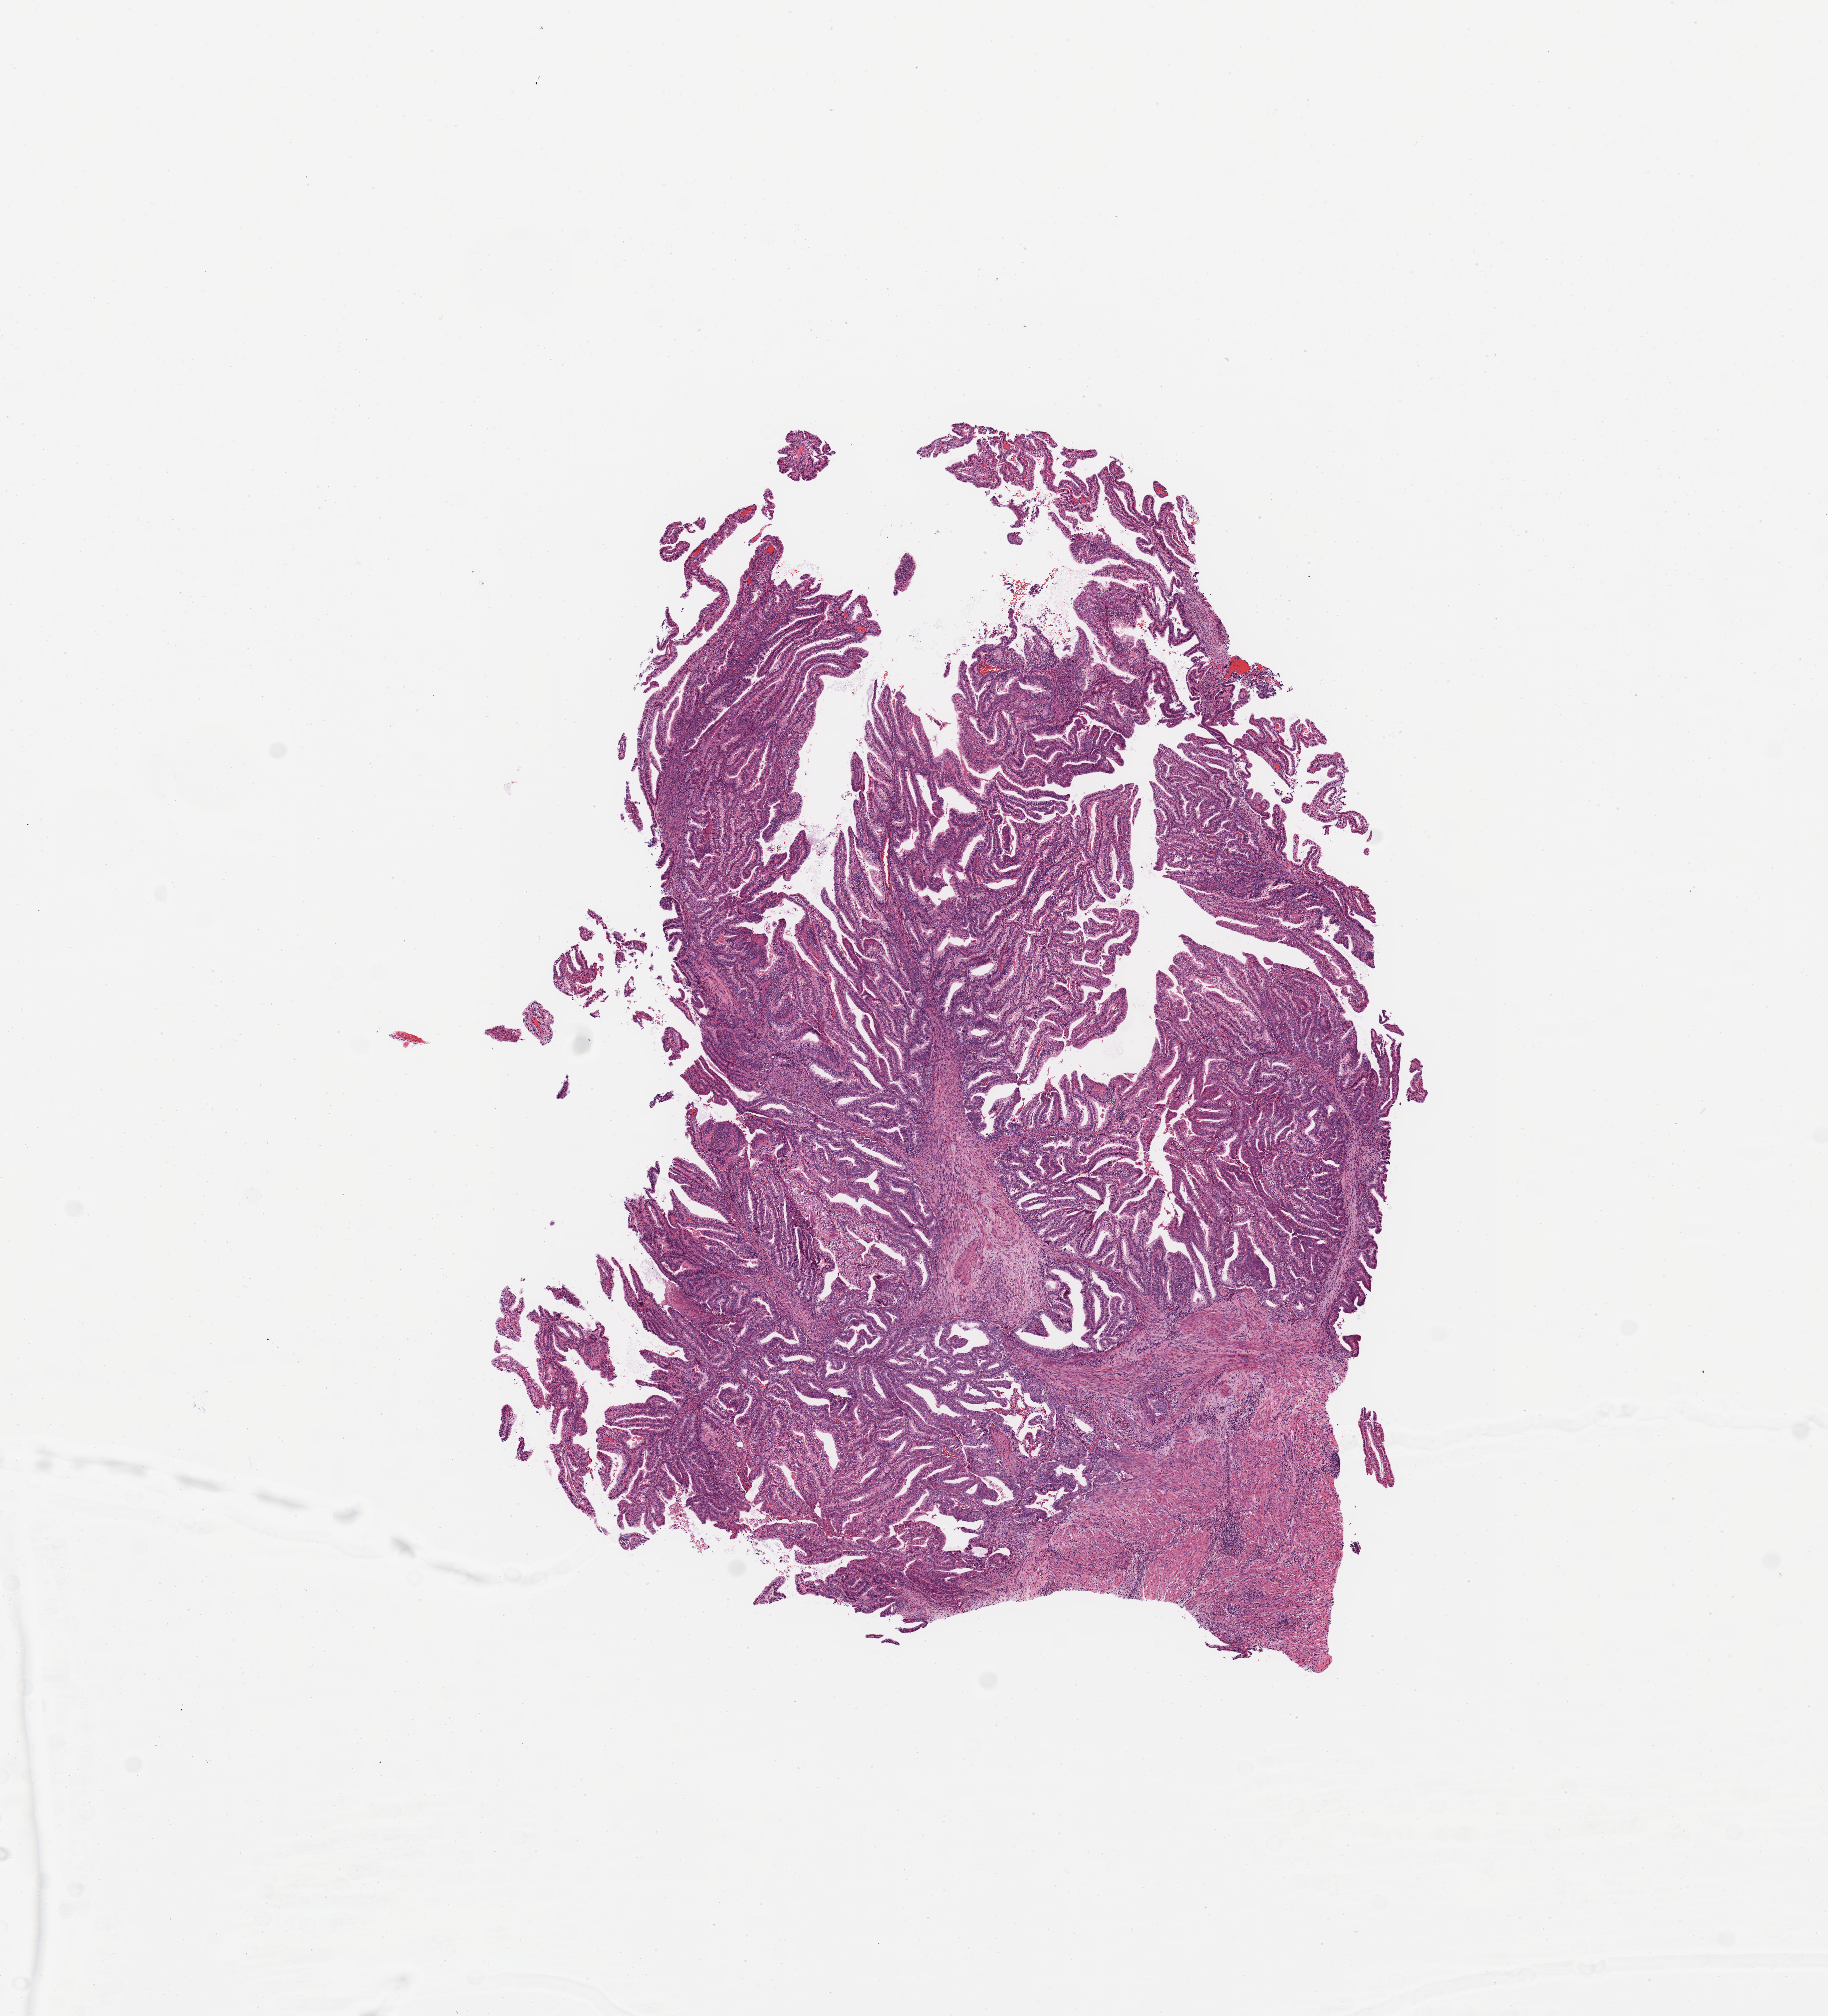
Hematoxylin and eosin (H&E) stained whole-slide image — low-resolution overview of the scanned area, about 10.8 x 11.9 mm, tumour tissue sample, sampled site: uterus. 55-year-old female patient. Histologic grade: high grade. Slide review estimates, as recorded: tumour nuclei 80%, necrosis 0%.
Diagnosis: Endometrioid adenocarcinoma, NOS. AJCC pathologic stage: IIIC1.